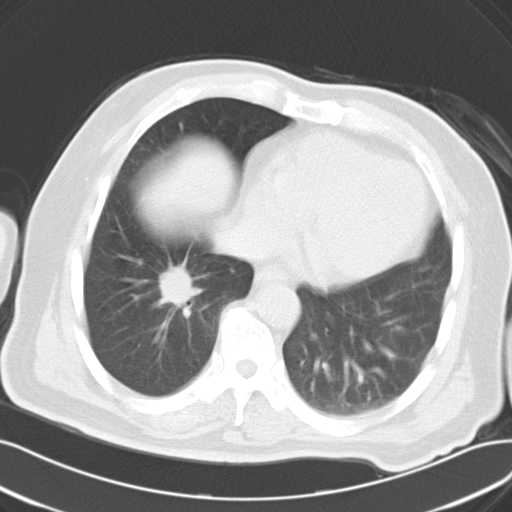
Chest CT, one axial slice. Slice 13 of 30 in the series (ordered by position). Reconstruction kernel B40f. 120 kVp. Lung window (W 1500 / L -600 HU). 10 mm slice thickness. 512 × 512 image matrix, field of view 363 × 363 mm. Male patient, age 69 years. Case-level facts recorded for this patient, not image findings: clinical TNM (as recorded): T1c N0 M0.
Outlined on this slice (bounding box drawn by a radiologist):
- lung tumour (recorded histology: adenocarcinoma): box from (x=147, y=249) to (x=207, y=317) px